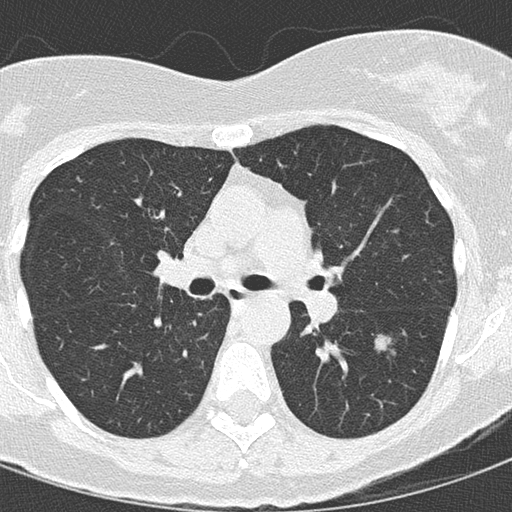
Chest CT (low-dose screening protocol), one axial image. Baseline annual screen. Lung window (W 1500 / L -600 HU). Slice 57 of 145 in the series. 512 × 512 image matrix, field of view 270 × 270 mm. Female, age 68 years at enrolment.
• Lesion marked by an expert reader, bounding box [x1, y1, x2, y2] px = [367, 321, 413, 367].
• The exam's reader record, not a measurement of the box and not confirmed to be the same lesion: non-calcified nodule or mass ≥4 mm, left lower lobe, 15 × 15 mm, mixed attenuation.
• Participant outcome: lung cancer diagnosed 72 days after this screen — bronchiolo-alveolar adenocarcinoma, NOS, left lower lobe, stage IIIB (AJCC 6th edition), 12 mm at pathology.